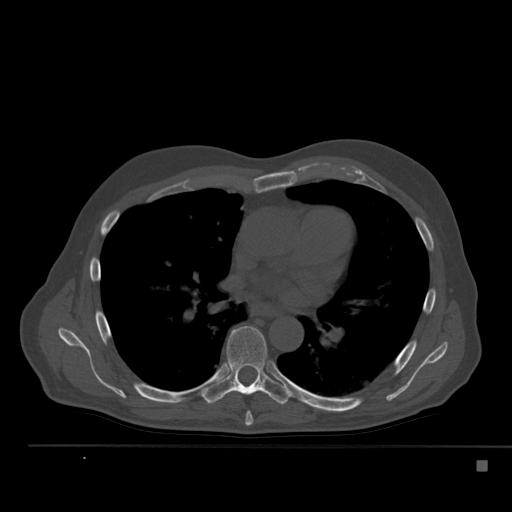
CT including the spine, one axial slice. Slice 332 of 517 in the series (ordered by position). Reconstruction kernel Br40s. Bone window (W 1800 / L 400 HU). 1.5 mm slice thickness. 512 × 512 image matrix. Patient: male, 70 years. From the clinical record (not read from this slice): primary cancer: renal.
Annotated regions visible in this slice (semi-automatically segmented with operator editing):
- T6 vertebra: bounding box (x1, y1, x2, y2) in pixels: (245, 412, 253, 426)
- T7 vertebra: (201, 326, 291, 405)